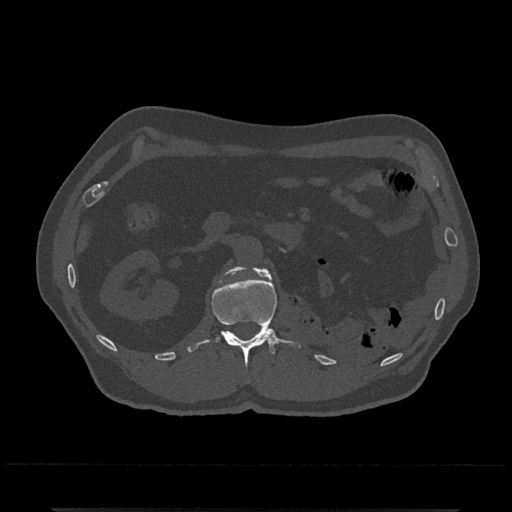
CT including the spine, one axial slice. Position 354 of 797 along the scan axis. Reconstruction kernel Br40s/3. 120 kVp. Bone window (W 1800 / L 400 HU). 0.5 mm slice thickness. 512 × 512 image matrix, field of view 393 × 393 mm. Patient: male, 67 years. Case-level facts recorded for this patient, not image findings: primary cancer: prostate.
Outlined on this slice (semi-automatically segmented with operator editing):
- L1 vertebra: box from (x=187, y=266) to (x=301, y=369) px